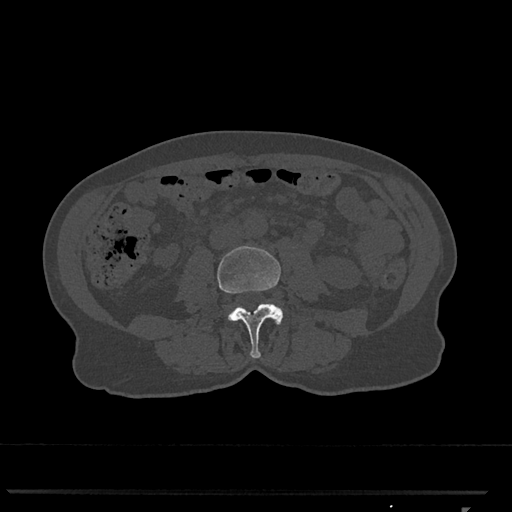
CT including the spine, one axial slice; position 260 of 793 along the scan axis; reconstruction kernel Br40s/3; bone window (W 1800 / L 400 HU); 512 × 512 image matrix. Female patient, age 62 years. Case-level facts recorded for this patient, not image findings: primary cancer: renal.
Outlined on this slice (semi-automatically segmented with operator editing):
- L3 vertebra: bounding box (x1, y1, x2, y2) in pixels: (217, 246, 283, 358)